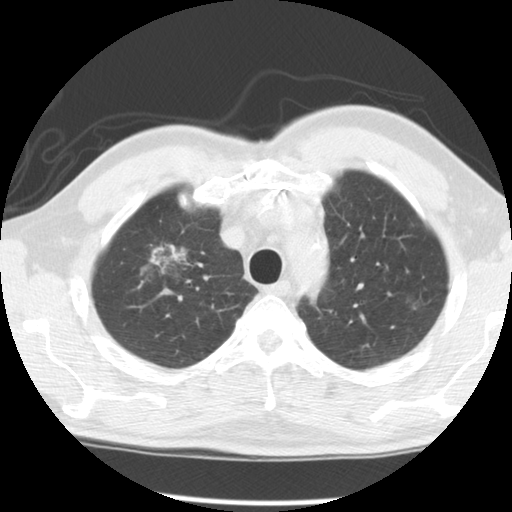
Low-dose screening chest CT, axial slice; second screening round (one year after baseline); lung window (W 1500 / L -600 HU); 2.5 mm slice thickness; standard (soft-tissue) reconstruction kernel (STANDARD); 120 kVp; slice 23 of 120 in the series. Male, age 64 years at enrolment. Former smoker at enrolment.
Lesion marked by an expert reader, bounding box (x1, y1, x2, y2) in pixels: (121, 221, 204, 296). The screening reader recorded 2 non-calcified nodules or masses ≥4 mm on this exam (right upper lobe, left upper lobe); which of them this box marks is not recorded. Later outcome: lung cancer diagnosed 429 days after this screen (after the third annual screen) — adenocarcinoma, NOS, right upper lobe, well differentiated (G1), stage IB (AJCC 6th edition), 45 mm at pathology.